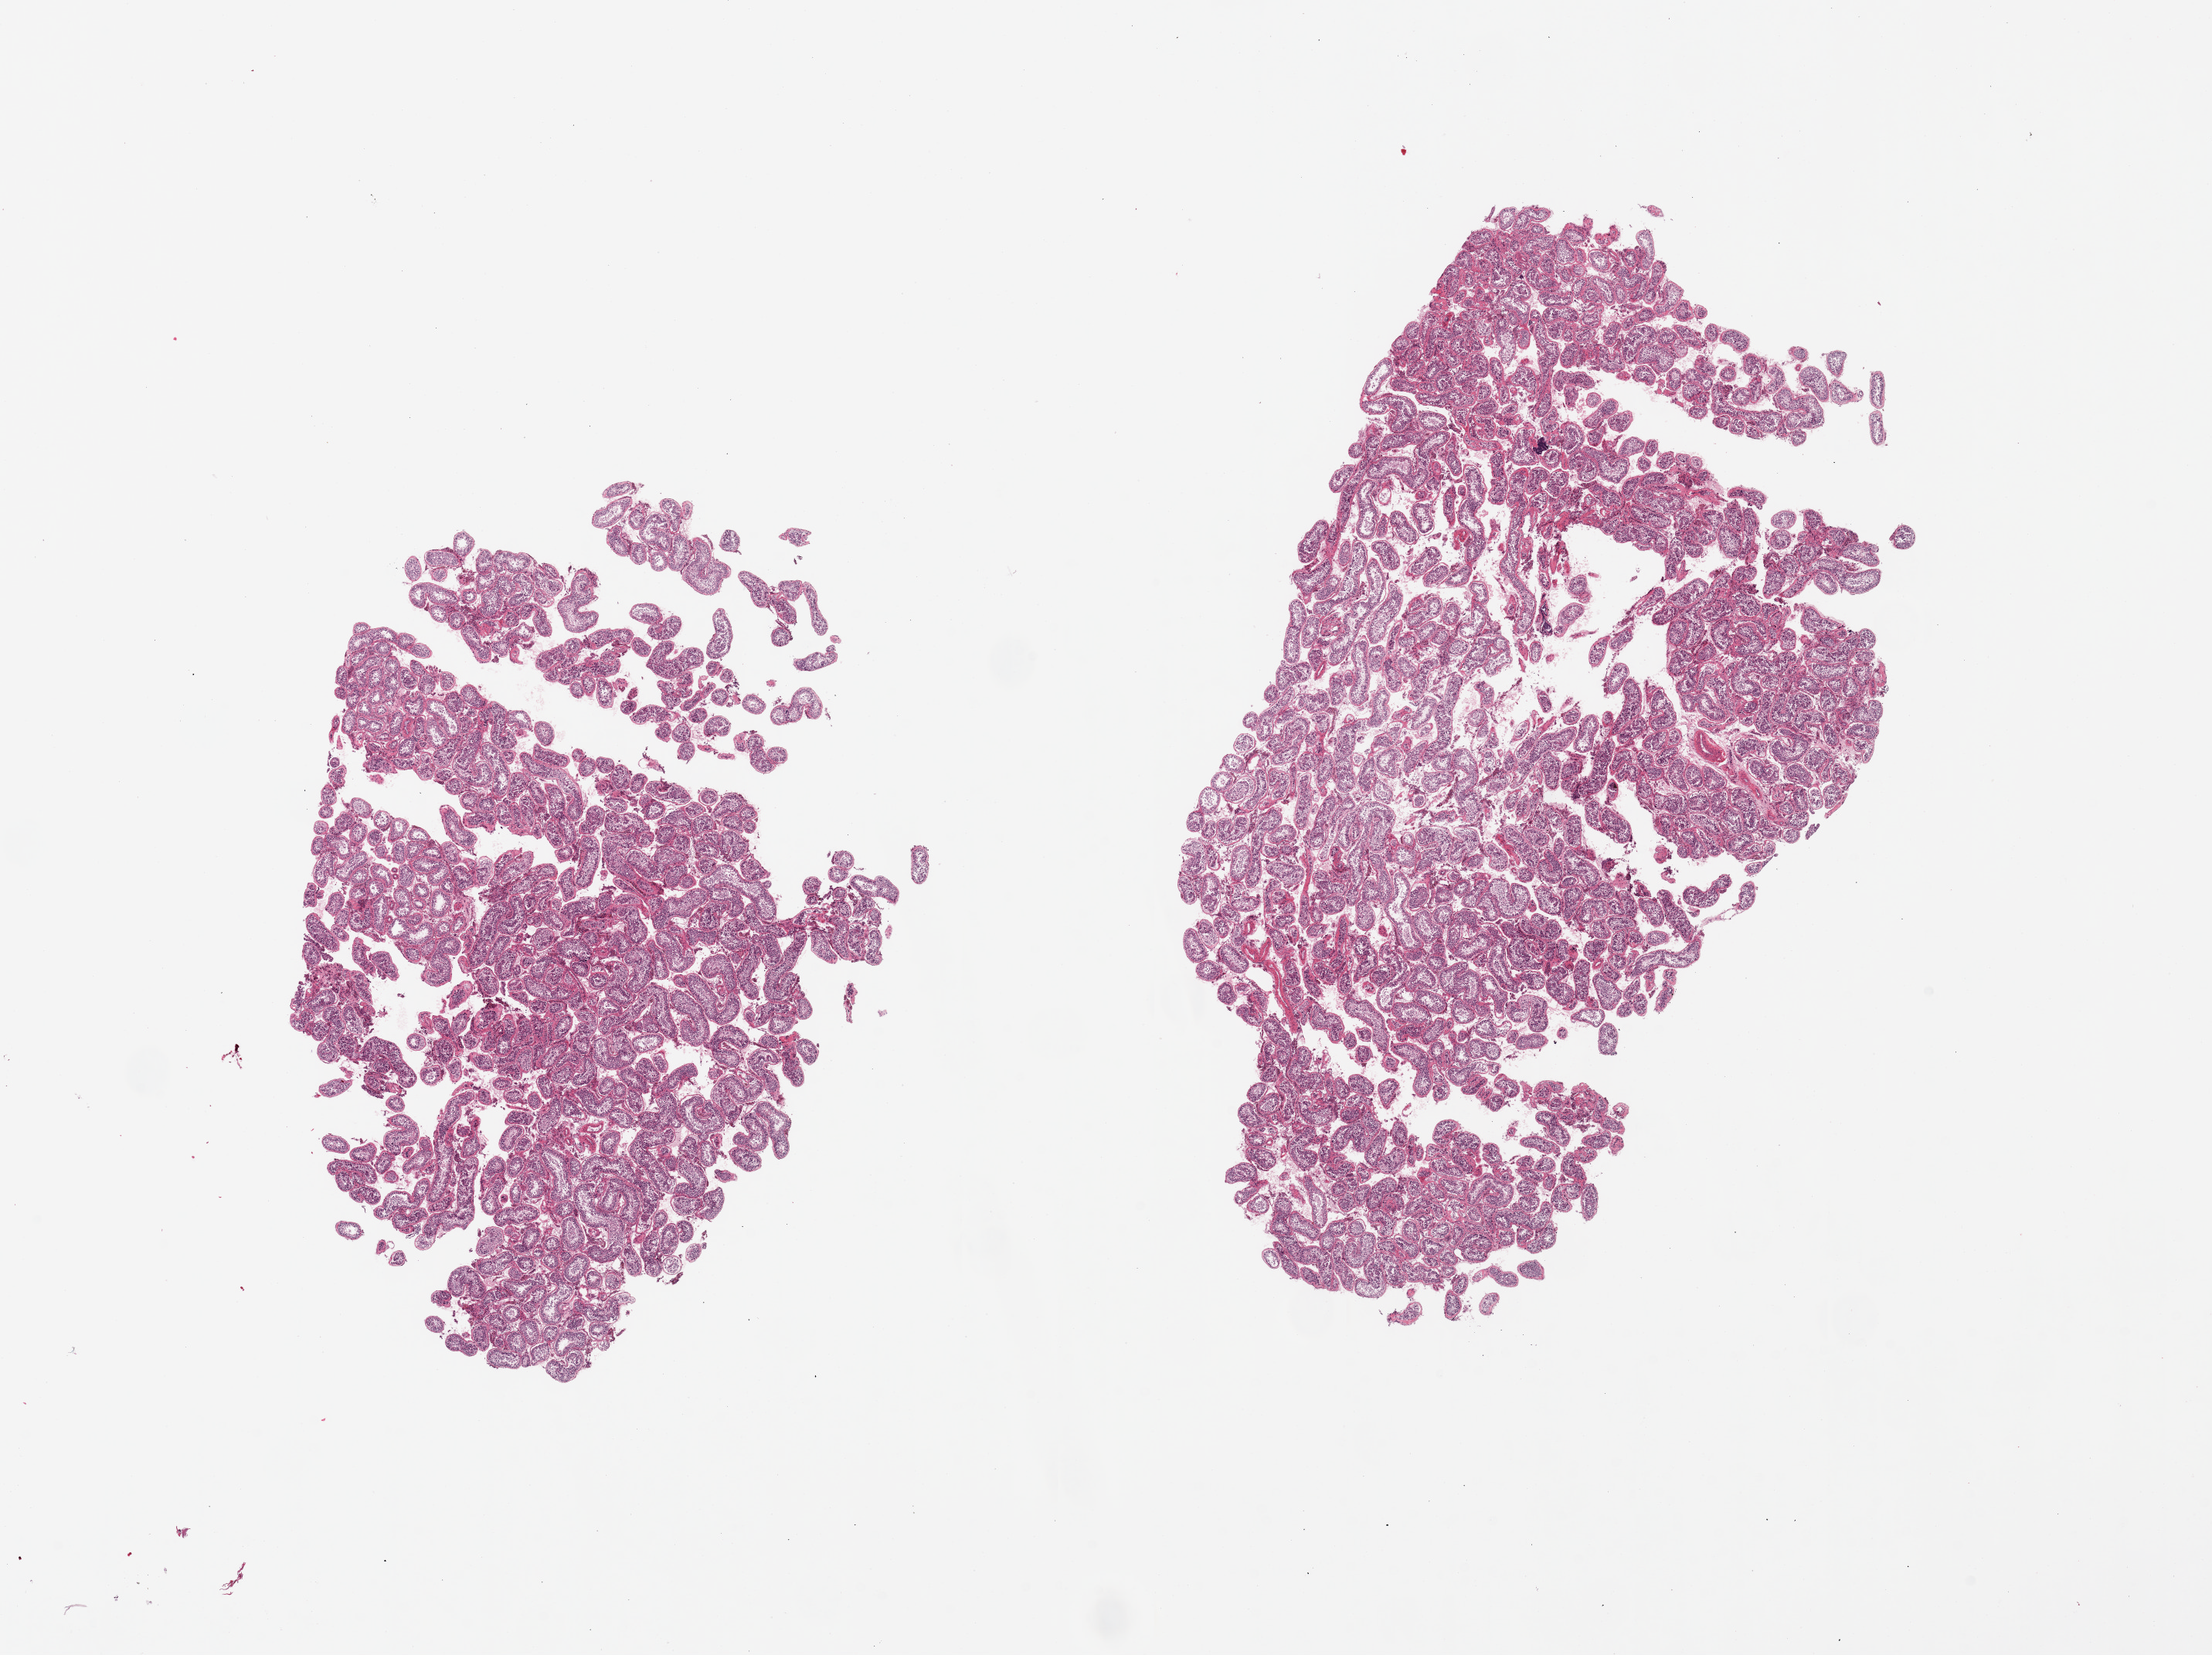
H&E whole-slide image, brightfield, low-resolution overview of the scanned area, about 22.6 x 16.9 mm (slide scanned at 20x). PAXgene-fixed paraffin-embedded (PFPE) section. Sampled site (target tissue): testis. Tissue donor sample.
Reviewer comment on this tissue sample: 2 pieces, well preserved; spermatogenesis is present.